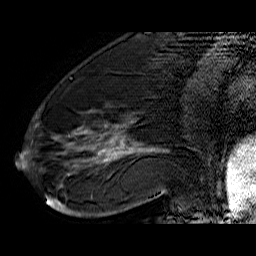
Breast MRI (dynamic contrast-enhanced), one sagittal slice; position 21 of 60 along the scan axis; dynamic contrast-enhanced series, time point 2 of 6 at this slice position (early post-contrast); 1.5 T; TE 6.4 ms, TR 32.9 ms; 4 mm slice thickness; 256 × 256 image matrix, field of view 200 × 200 mm. Female patient. From the clinical record (not read from this slice): setting: breast cancer imaged before/during neoadjuvant chemotherapy; receptor status: HR-positive, HER2-negative.
Outlined on this slice (semi-automatic segmentation, software-assisted and operator-edited):
- analysis volume of interest (the breast-tissue region the enhancement analysis was run in; not a lesion): bounding box (x1, y1, x2, y2) in pixels: (46, 74, 176, 210)
- tumour enhancement mask (voxels above the 100 % enhancement threshold inside the analysis volume of interest): (47, 127, 168, 209)